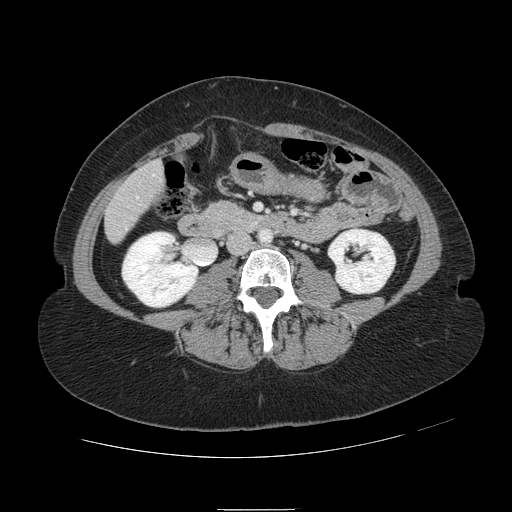
Contrast-enhanced abdominal CT, one axial slice. Slice 13 of 121 in the series (ordered by position). 120 kVp. Intravenous contrast given. Soft-tissue window (W 400 / L 40 HU). 512 × 512 image matrix. Female patient, age 52 years. From the clinical record (not read from this slice): diagnosis: colorectal cancer liver metastases, imaged before liver resection; multiple liver metastases: yes; largest metastasis: 6.3 cm.
Annotated regions visible in this slice (expert manual segmentation):
- hepatic veins: box from (x=118, y=175) to (x=154, y=235) px
- liver: (x=106, y=163)–(x=164, y=241)